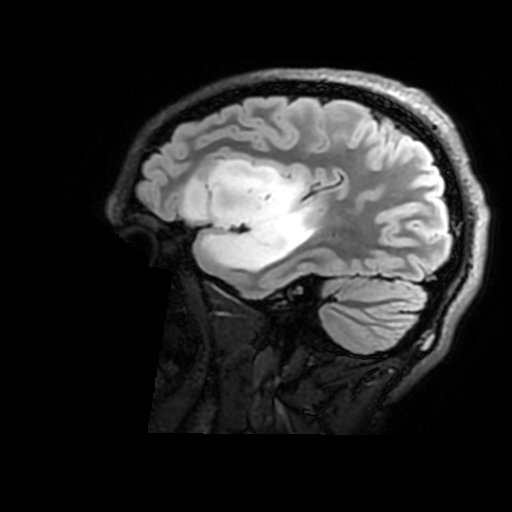
Brain MRI from a brain-tumour surgery series, one sagittal slice; slice 127 of 176 in the series (ordered by position); T2 FLAIR; 1 mm slice thickness; 512 × 512 image matrix, field of view 240 × 240 mm. Case-level facts recorded for this patient, not image findings: histopathology: Astrocytoma; WHO grade: 2; IDH mutation: yes.
Outlined on this slice (outlined manually by an expert reader):
- tumour: bounding box [x1, y1, x2, y2] px = [184, 157, 314, 273]